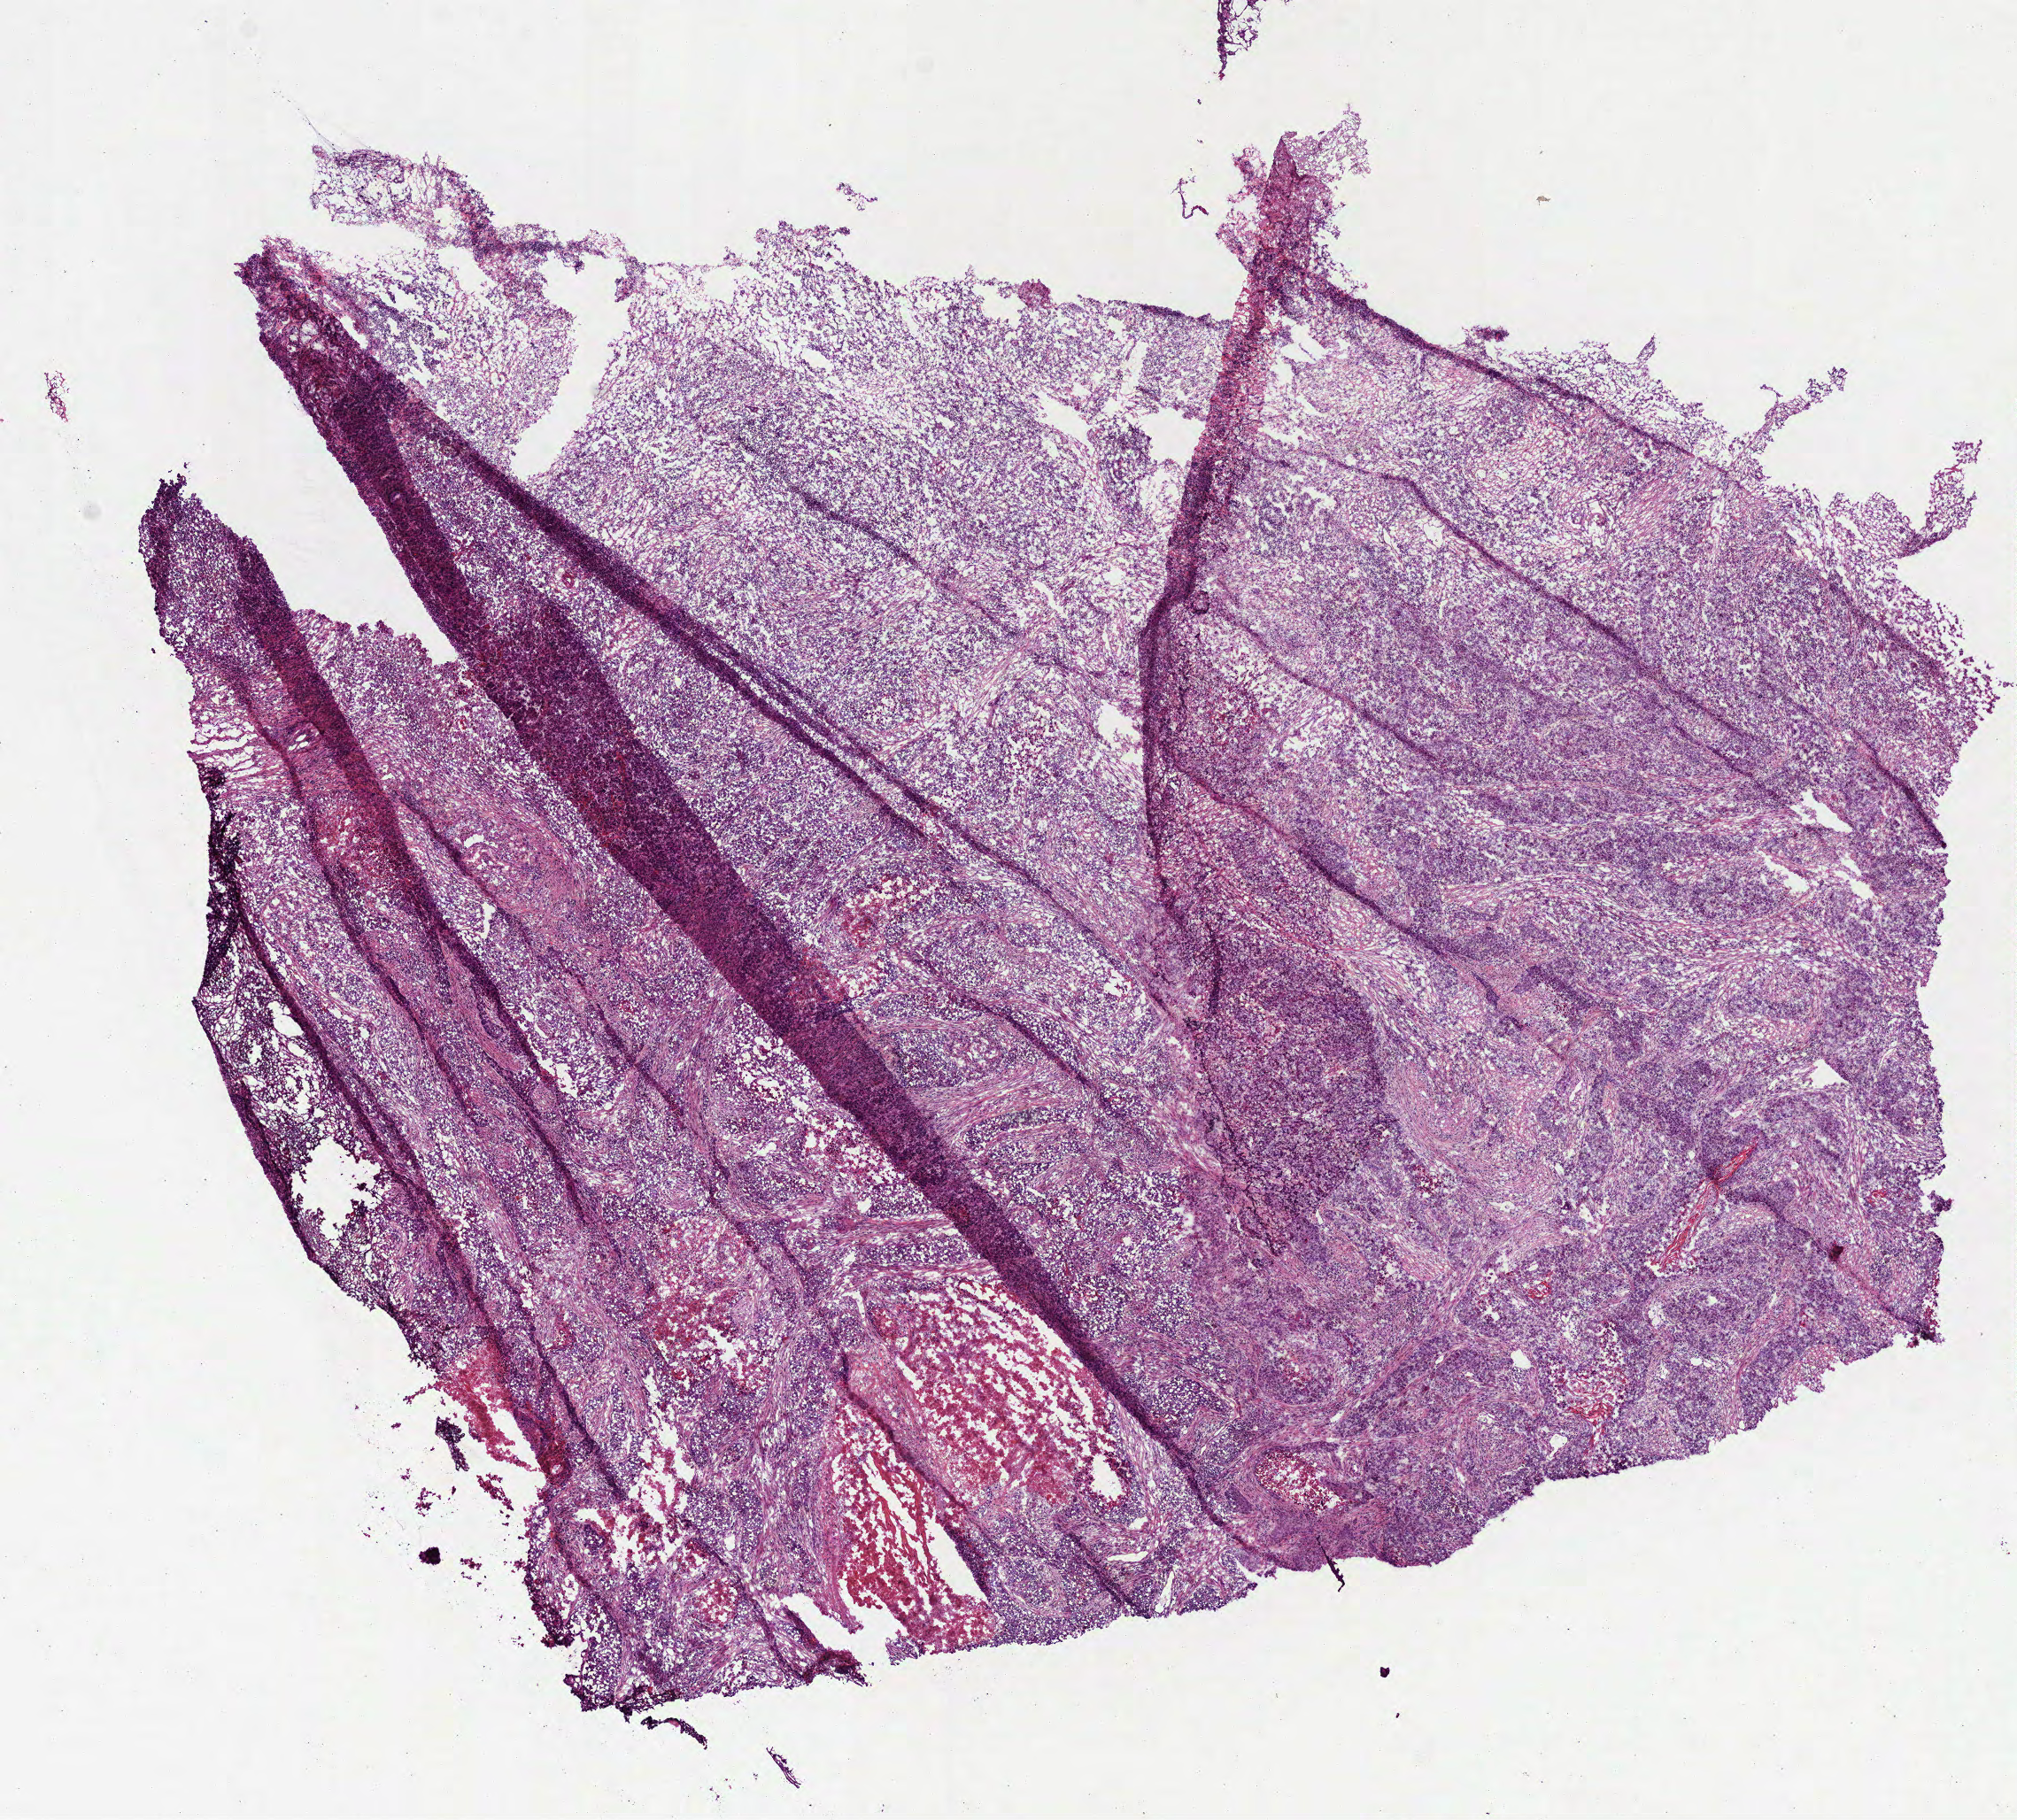
Whole-slide histology image, H&E, a low-resolution overview of the entire scanned area, about 9.2 x 8.3 mm (acquisition: 40x scan), frozen section from the bottom of the tissue portion, primary tumour sample from the lung. Male, age 62 years at initial diagnosis. Slide review estimates, as recorded: tumour cells 67%, tumour nuclei 65%, normal cells 0%, stromal cells 25%, necrosis 8%.
AJCC pathologic stage: IIA. Histologic diagnosis: Squamous cell carcinoma, NOS (upper lobe, lung).